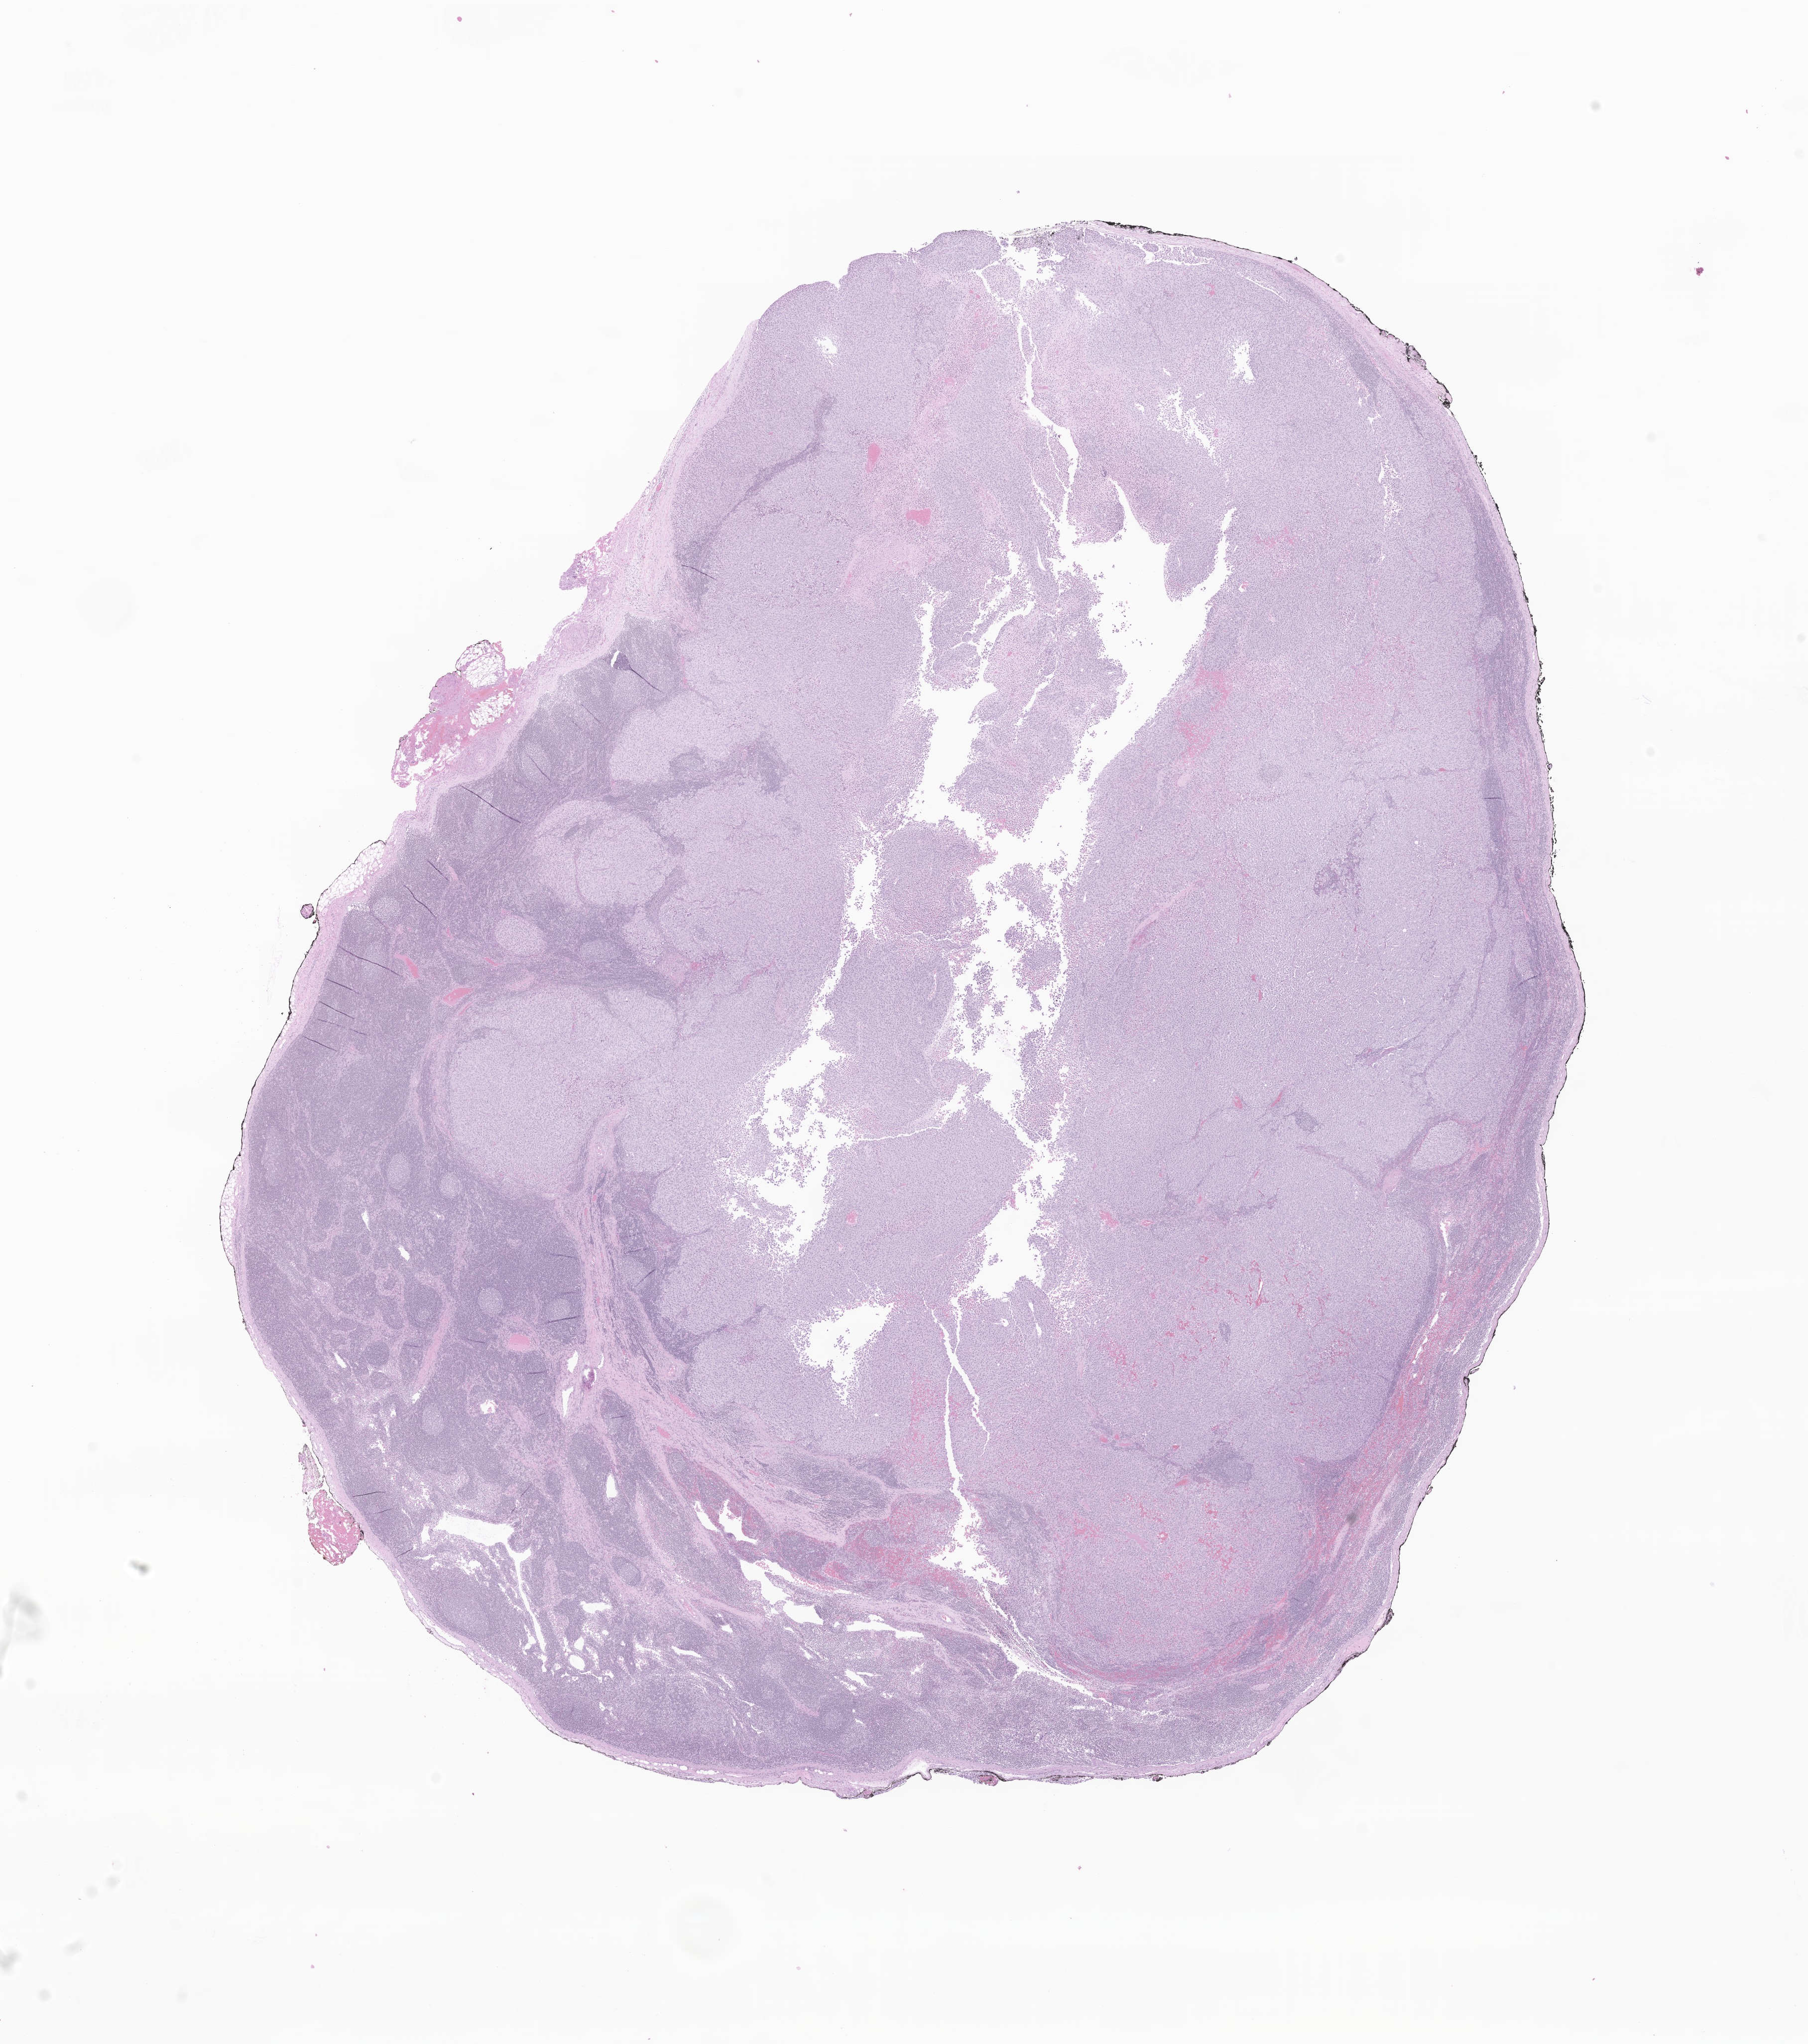
Digitized hematoxylin and eosin (H&E)-stained section of tumor tissue from the skin of upper limb — whole scanned area (about 15.3 x 17.3 mm) shown as a low-resolution overview, formalin-fixed, paraffin-embedded (FFPE) tissue. Patient male; age 178 months.
Diagnosis: Nodular melanoma.